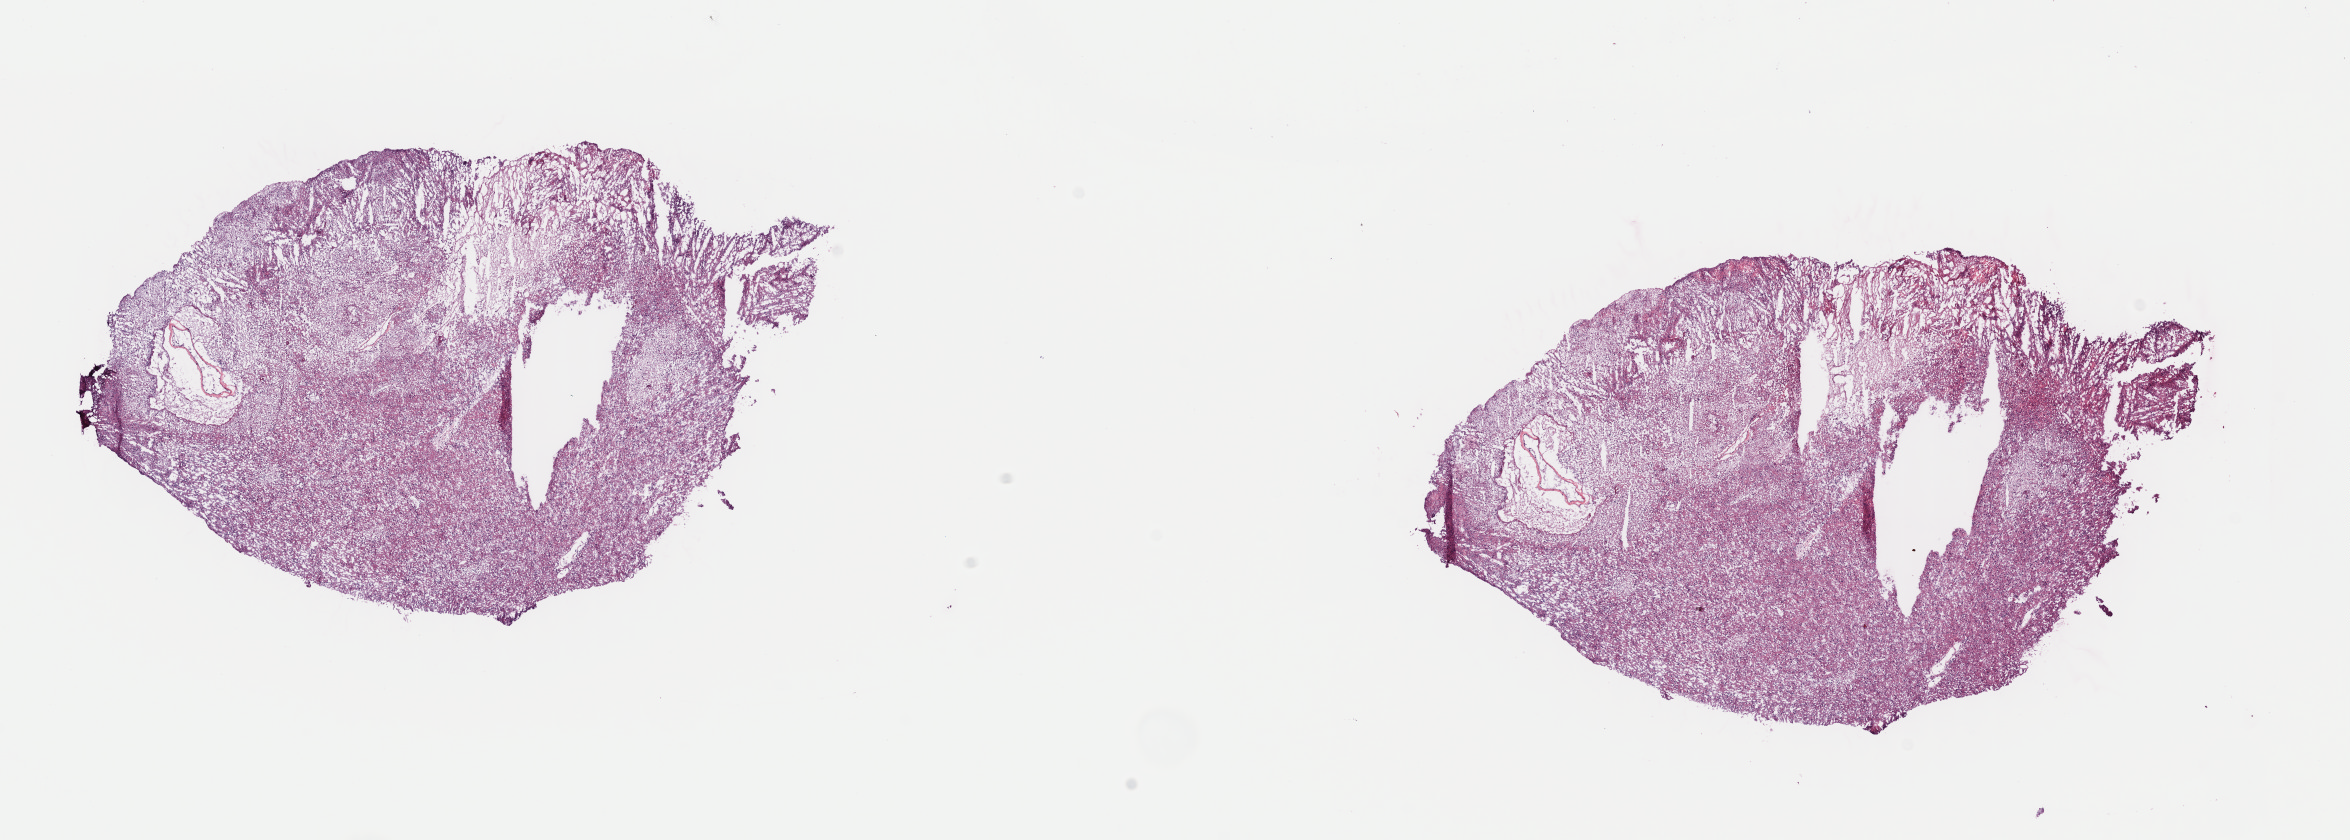
Whole-slide histology image, H&E-stained, shown as a low-resolution overview of the whole scanned area (about 18.5 x 6.6 mm), frozen section from the top of the tissue portion, sample: primary tumour, brain. Female patient; age at initial diagnosis 37 years.
Histologic diagnosis: Oligodendroglioma, NOS (cerebrum).